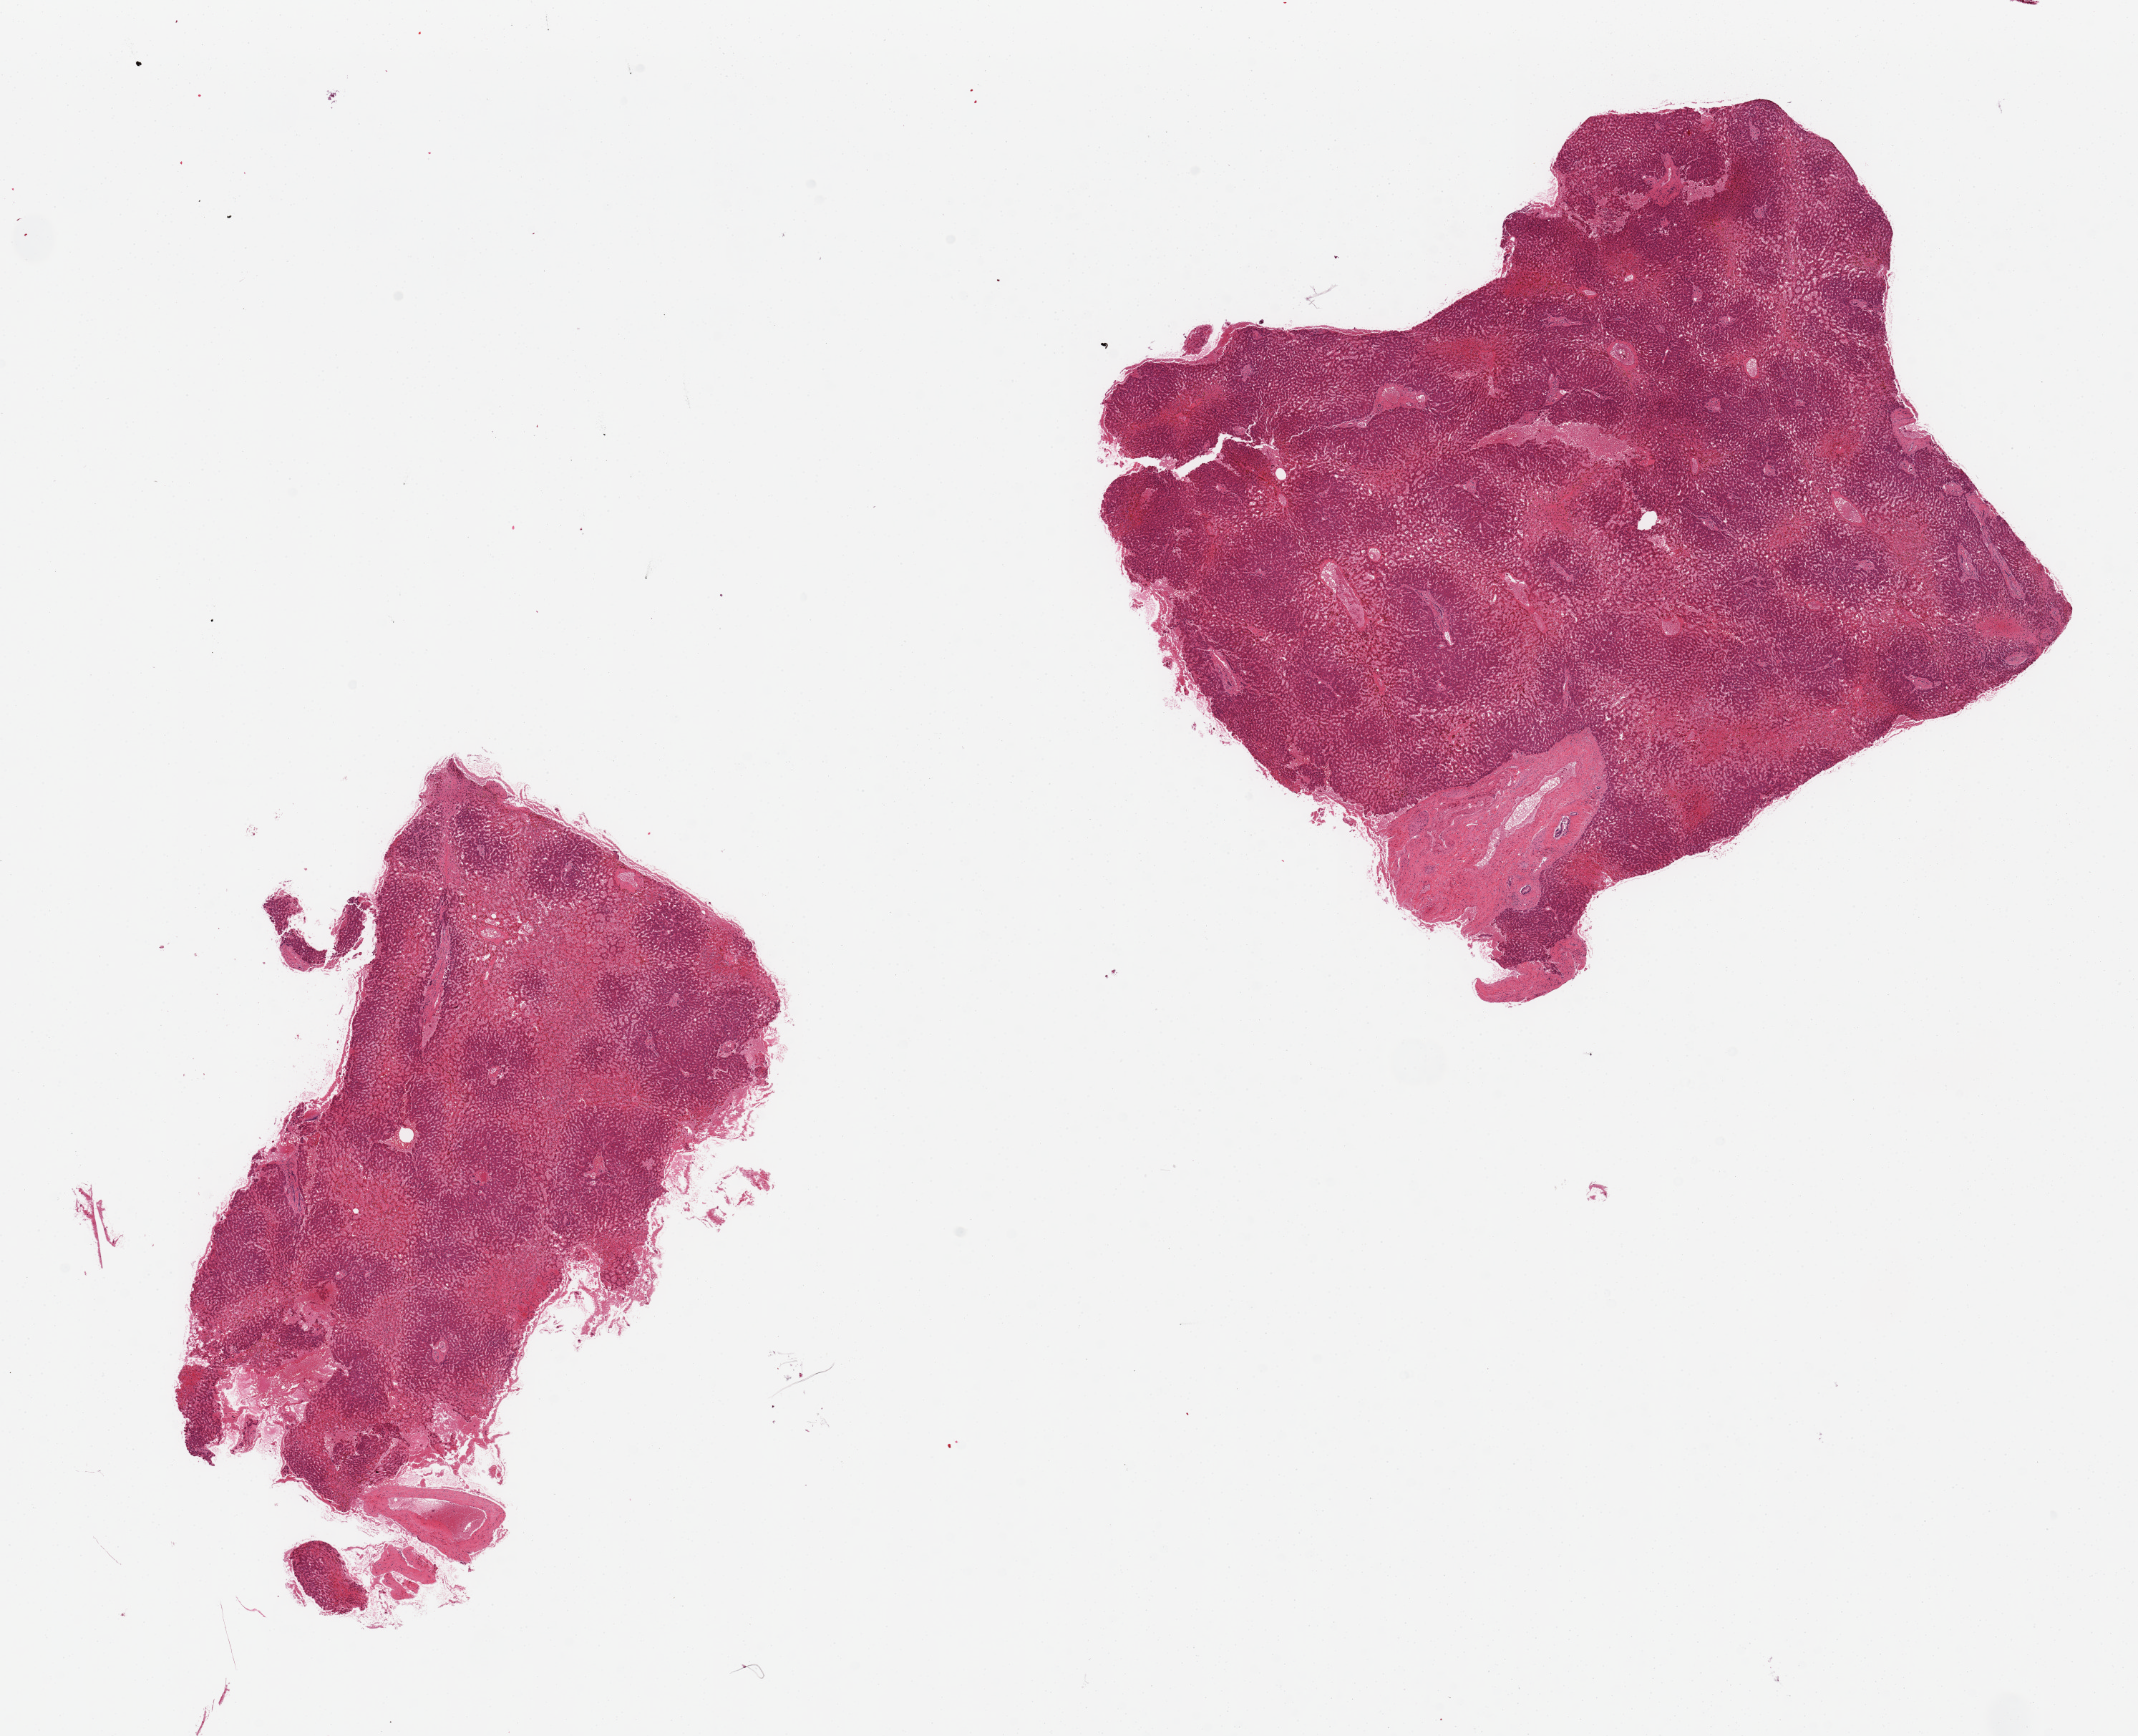
Whole-slide image, hematoxylin and eosin (H&E) stain, brightfield, a low-resolution overview of the entire scanned area, about 23.6 x 19.2 mm (from a 20x scan), PAXgene-fixed paraffin-embedded (PFPE) section, sampled site (target tissue): liver, donor tissue sample. Female donor.
* pathologist's review note for this sample: 2 pieces, severe passive congestion, mild steatosis (~10%)